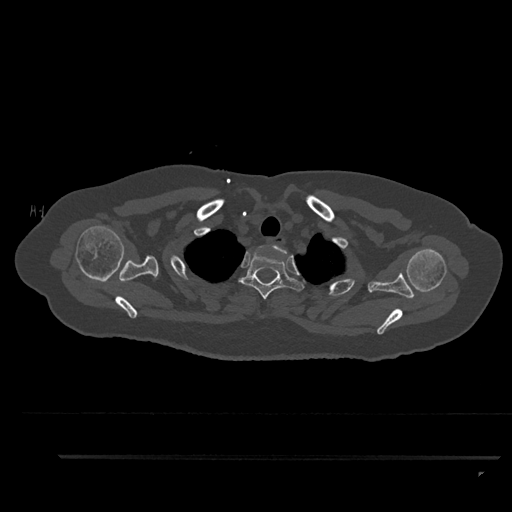
CT including the spine, one axial slice. Position 728 of 797 along the scan axis. Reconstruction kernel Br40s/3. Bone window (W 1800 / L 400 HU). 0.5 mm slice thickness. 512 × 512 image matrix, field of view 408 × 408 mm. Female patient, age 44 years. Case-level facts recorded for this patient, not image findings: primary cancer: renal; vertebrae with lytic lesions (as recorded): L1.
Outlined on this slice (semi-automatically segmented with operator editing):
- T1 vertebra: bounding box (x1, y1, x2, y2) in pixels: (260, 245, 287, 253)
- T2 vertebra: (238, 250, 304, 300)